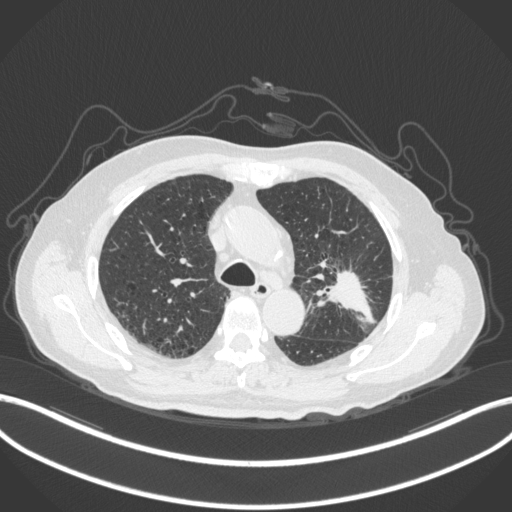
Chest CT, one axial slice; position 201 of 331 along the scan axis; reconstruction kernel B31f; lung window (W 1500 / L -600 HU); 1 mm slice thickness; 512 × 512 image matrix, field of view 400 × 400 mm. Patient: male, 79 years. From the clinical record (not read from this slice): clinical TNM (as recorded): T2a N1 M1; histopathological grade: G3.
Annotated regions visible in this slice (rectangle marked by the reading radiologist):
- lung tumour (recorded histology: adenocarcinoma): bounding box [x1, y1, x2, y2] px = [318, 264, 379, 328]